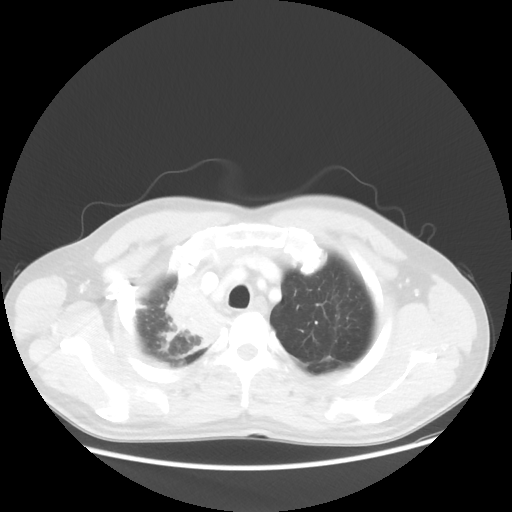
Chest CT, one axial slice; slice 46 of 56 in the series (ordered by position); reconstruction kernel STANDARD; 100 kVp; lung window (W 1500 / L -600 HU); 5 mm slice thickness; 512 × 512 image matrix. Male patient, age 60 years. Case-level facts recorded for this patient, not image findings: clinical TNM (as recorded): T2a N1 M0.
Structures marked on this image (rectangle marked by the reading radiologist):
- lung tumour (recorded histology: squamous cell carcinoma): bounding box <145,266,225,356> (left, top, right, bottom; pixels)